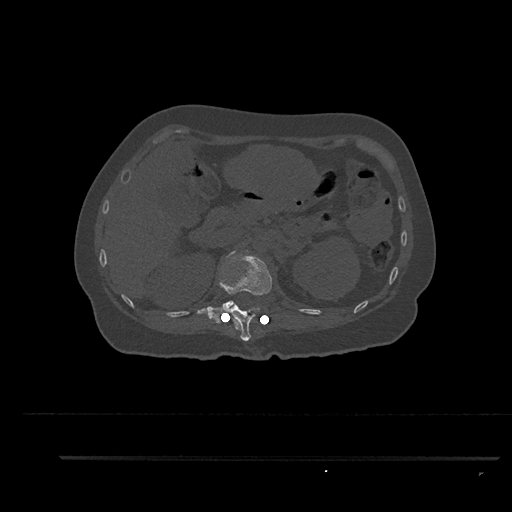
CT including the spine, one axial slice; position 242 of 797 along the scan axis; reconstruction kernel Br40s/3; bone window (W 1800 / L 400 HU); 512 × 512 image matrix. Patient: female, 44 years. Case-level facts recorded for this patient, not image findings: primary cancer: renal; vertebrae with lytic lesions (as recorded): L1.
Annotated regions visible in this slice (semi-automatically segmented with operator editing):
- L1 vertebra: box from (x=219, y=250) to (x=249, y=309) px
- T12 vertebra: (x=202, y=251)–(x=272, y=341)